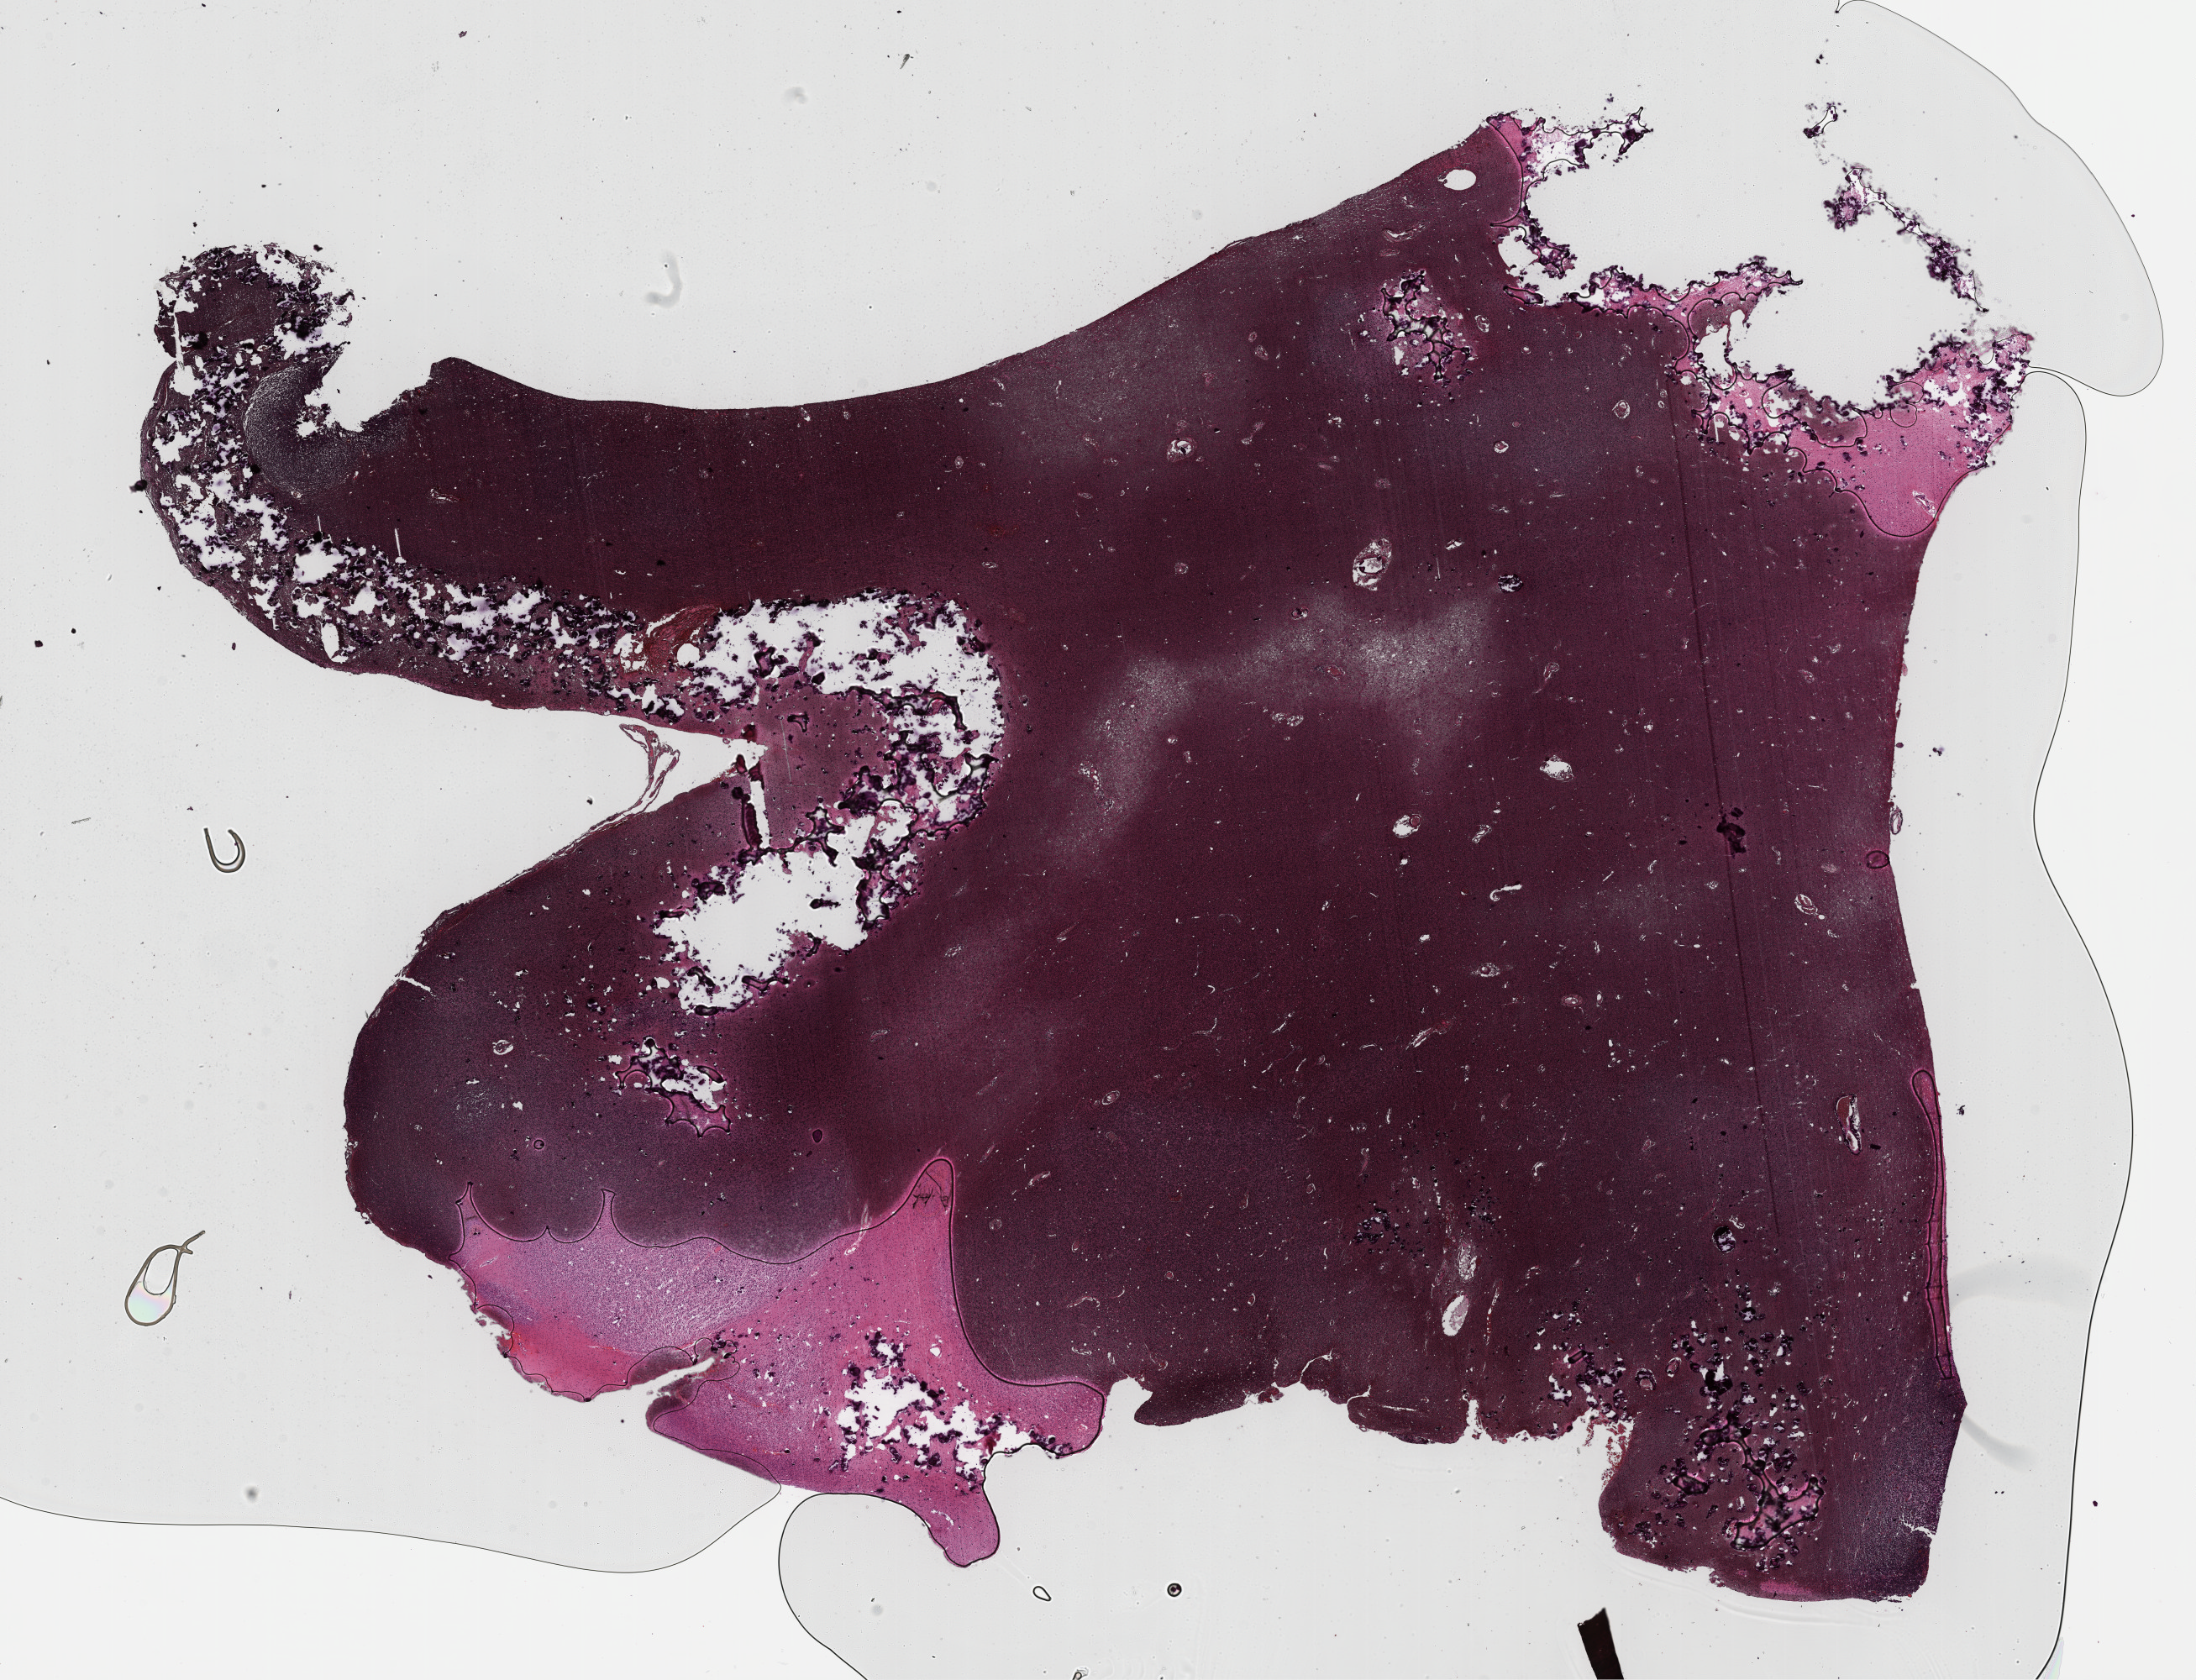
Digitized H&E tissue section (whole slide), a low-resolution overview of the entire scanned area, about 21.1 x 16.2 mm; formalin-fixed paraffin-embedded (FFPE) diagnostic section; sample: primary tumour, brain. Patient: male, age at initial diagnosis 53 years. Histologic grade: G3 (poorly differentiated).
• diagnosis: Oligodendroglioma, anaplastic (cerebrum)